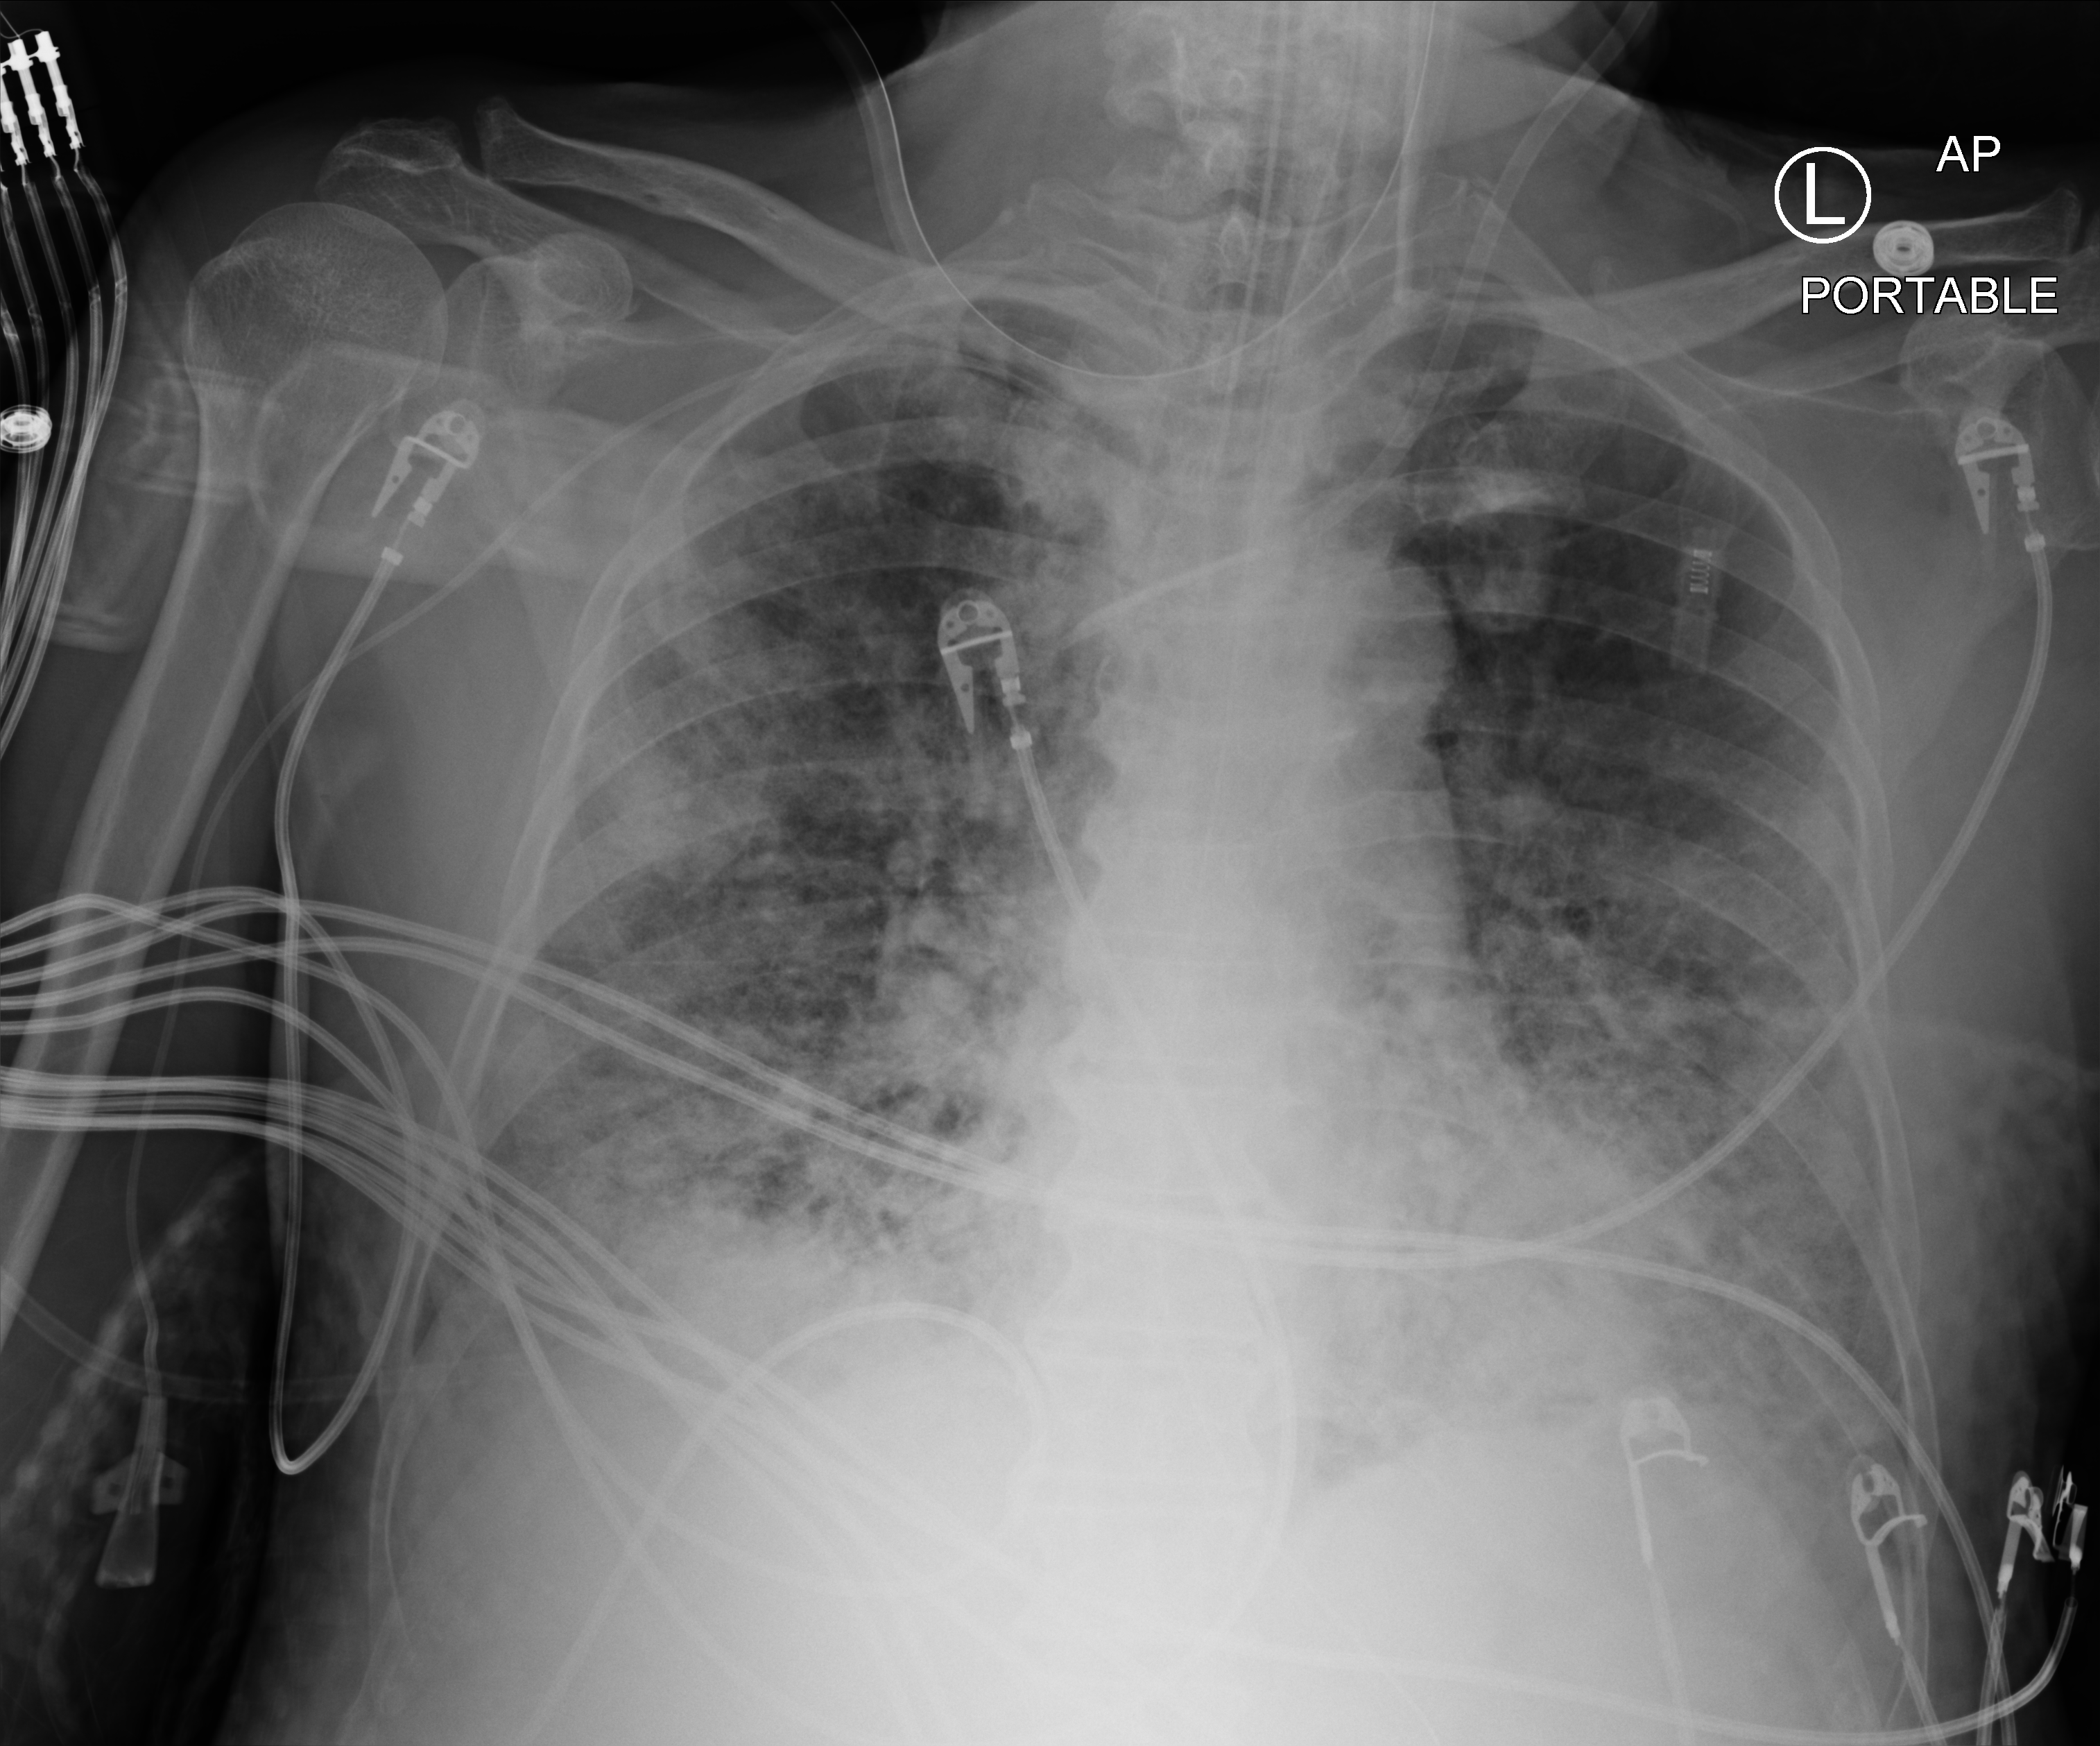
Chest X-ray (portable); anteroposterior (AP) projection. Male patient hospitalised with COVID-19, age 60–74 years.
From the hospital-stay record, not from the radiograph (when in the stay this image was taken is not recorded):
- admitted to intensive care during this hospital stay: yes
- chronic kidney disease (admission record): no